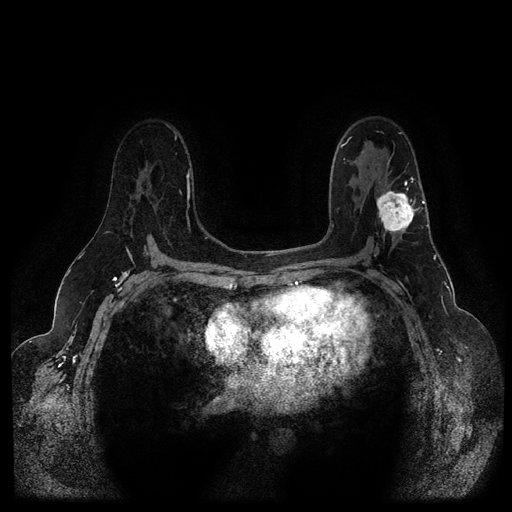
Breast MRI (dynamic contrast-enhanced, multi-phase), one axial slice. Slice 65 of 116 in the series (ordered by position). Dynamic contrast-enhanced series, time point 2 of 5 at this slice position (early post-contrast). 1.5 T. TE 2.6 ms, TR 5.3 ms. 2 mm slice thickness. 512 × 512 image matrix, field of view 350 × 350 mm. Patient: female, 54 years.
Annotated regions visible in this slice (semi-automatically segmented with operator editing):
- breast lesion (labelled 'tumour' in the annotation; benign lesions carry a separate 'benign' label): bounding box <375,190,419,235> (left, top, right, bottom; pixels)